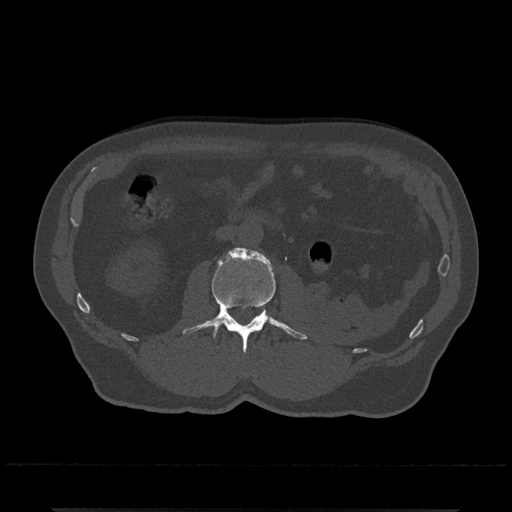
CT including the spine, one axial slice; slice 288 of 797 in the series (ordered by position); reconstruction kernel Br40s/3; bone window (W 1800 / L 400 HU); 0.5 mm slice thickness; 512 × 512 image matrix, field of view 393 × 393 mm. Male patient, age 67 years. From the clinical record (not read from this slice): primary cancer: prostate.
Annotated regions visible in this slice (semi-automatically segmented with operator editing):
- L2 vertebra: bounding box [x1, y1, x2, y2] px = [183, 248, 307, 353]